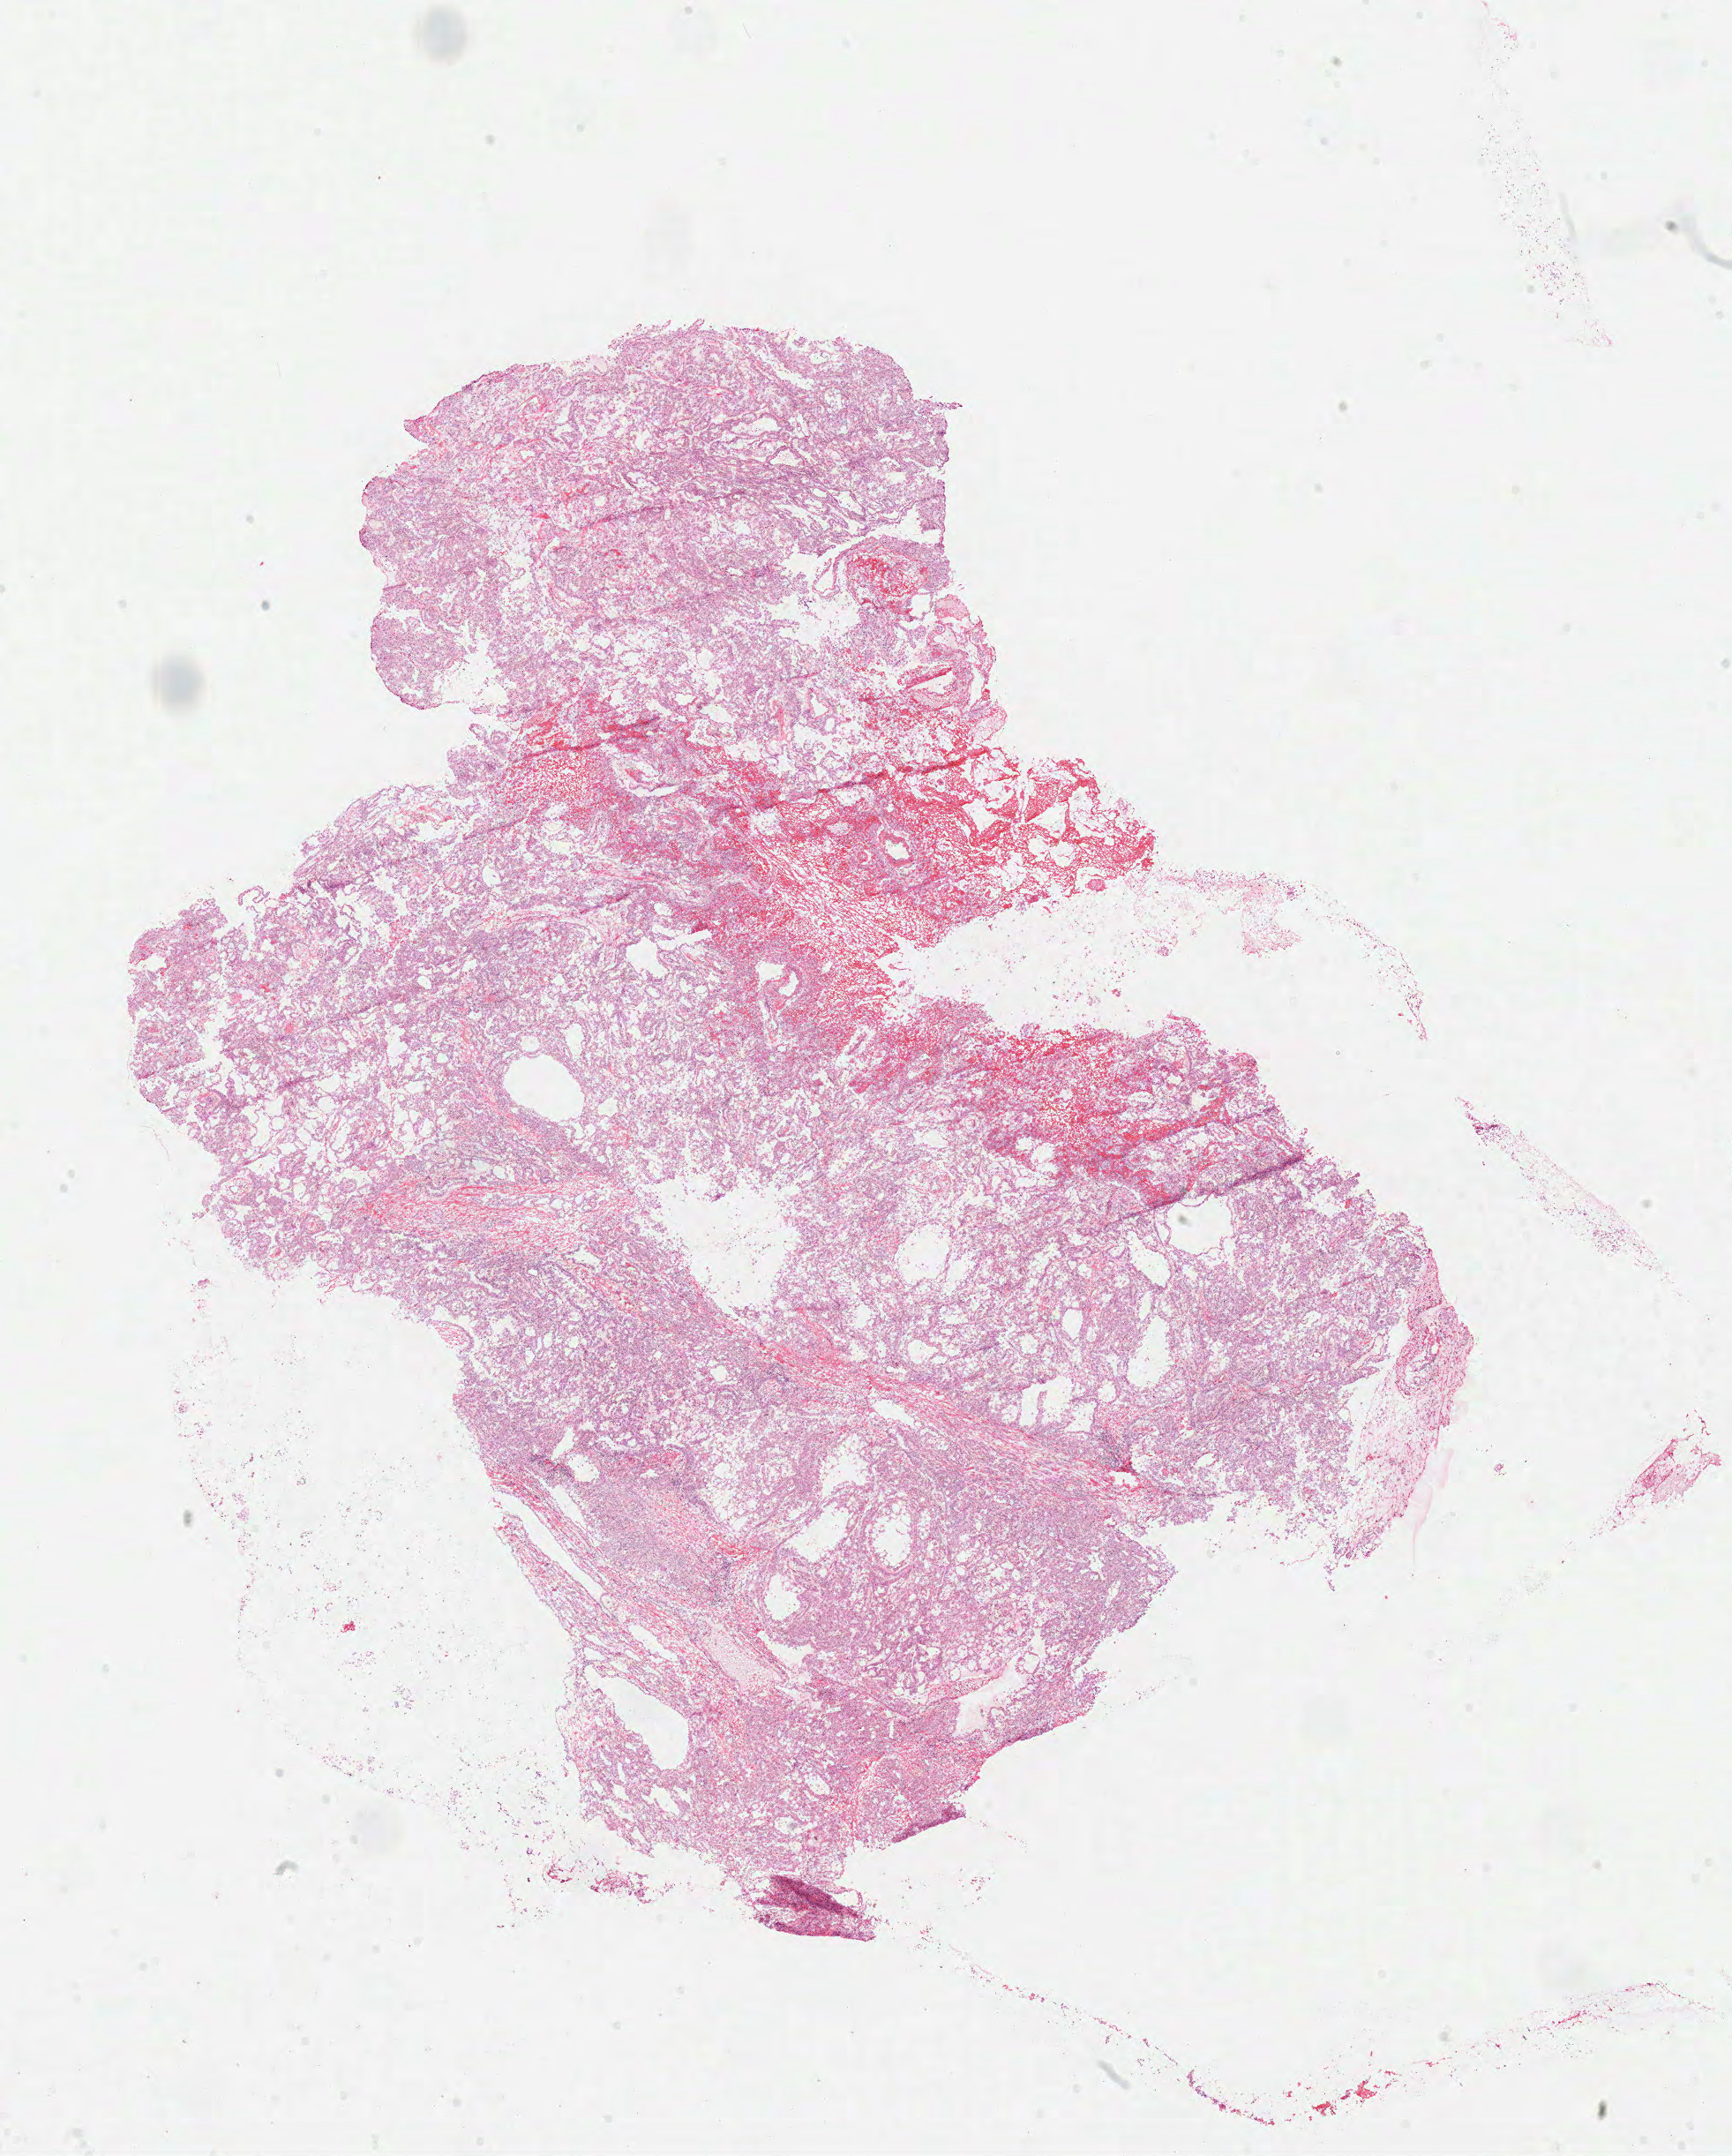
Whole-slide histology image, H&E-stained, shown as a low-resolution overview of the whole scanned area (about 15.5 x 19.3 mm, acquisition: 40x scan), frozen section from the top of the tissue portion, sample: primary tumour, kidney. Female patient; age at initial diagnosis 32 years. Slide review estimates, as recorded: tumour cells 80%, tumour nuclei 80%, normal cells 0%, stromal cells 10%, necrosis 10%.
- AJCC pathologic stage: III
- TNM: T3b N1 M0
- diagnosis: Papillary adenocarcinoma, NOS